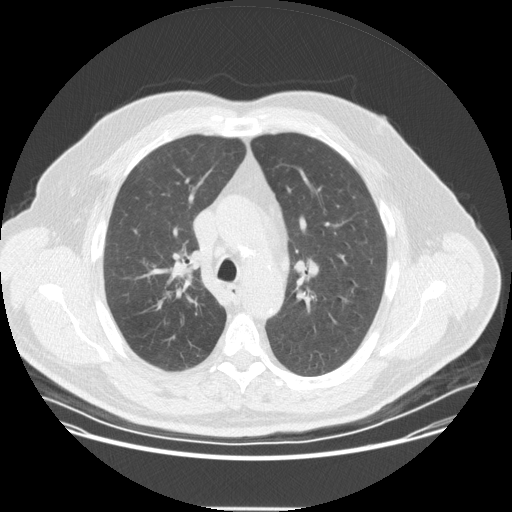
Low-dose screening chest CT, one axial slice. Position 238 of 351 along the scan axis. Reconstruction kernel STANDARD. 120 kVp. Lung window (W 1500 / L -600 HU). 2.5 mm slice thickness. 512 × 512 image matrix.
Structures marked on this image (expert manual segmentation):
- lesion 1 (tumor, upper lobe of right lung): bounding box [x1, y1, x2, y2] px = [171, 267, 194, 287]